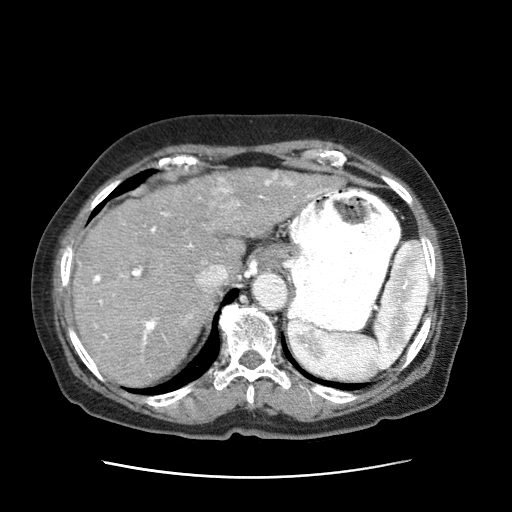
Contrast-enhanced abdominal CT (liver protocol), one axial slice; reconstruction kernel STANDARD; intravenous contrast given; soft-tissue window (W 400 / L 40 HU); 2.5 mm slice thickness; 512 × 512 image matrix. Female patient, age 79 years. Case-level facts recorded for this patient, not image findings: diagnosis: hepatocellular carcinoma (patient treated with transarterial chemoembolisation; whether this scan precedes or follows treatment is not stated here); TNM stage (as recorded): Stage-II; Child-Pugh class: B; tumour differentiation: well differentiated; tumour nodularity: multinodular.
Outlined on this slice (semi-automatic segmentation, software-assisted and operator-edited):
- abdominal aorta: bounding box (x1, y1, x2, y2) in pixels: (252, 272, 287, 311)
- liver parenchyma outside the tumour (the mass and vessels are separate outlines, so this box may not span the whole liver): (73, 183, 246, 389)
- mass: (187, 169, 344, 236)
- liver vessels: (93, 195, 296, 361)